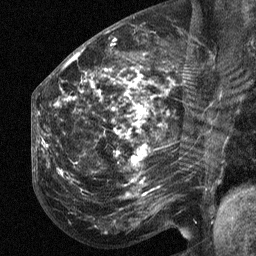
Breast MRI (dynamic contrast-enhanced), one sagittal slice; slice 28 of 64 in the series (ordered by position); dynamic contrast-enhanced study with each time point stored as its own series, time point 2 of 3 at this slice position (early post-contrast, ordered by acquisition time); 1.5 T; TE 4.8 ms, TR 27 ms; 2.3 mm slice thickness; 256 × 256 image matrix, field of view 200 × 200 mm. Patient: female, 50 years. From the clinical record (not read from this slice): setting: breast cancer imaged before/during neoadjuvant chemotherapy; receptor status: HER2-positive.
Annotated regions visible in this slice (semi-automatically segmented with operator editing):
- analysis volume of interest (the breast-tissue region the enhancement analysis was run in; not a lesion): bounding box [x1, y1, x2, y2] px = [53, 64, 211, 216]
- tumour enhancement mask (voxels above the 90 % enhancement threshold inside the analysis volume of interest): [105, 69, 148, 181]